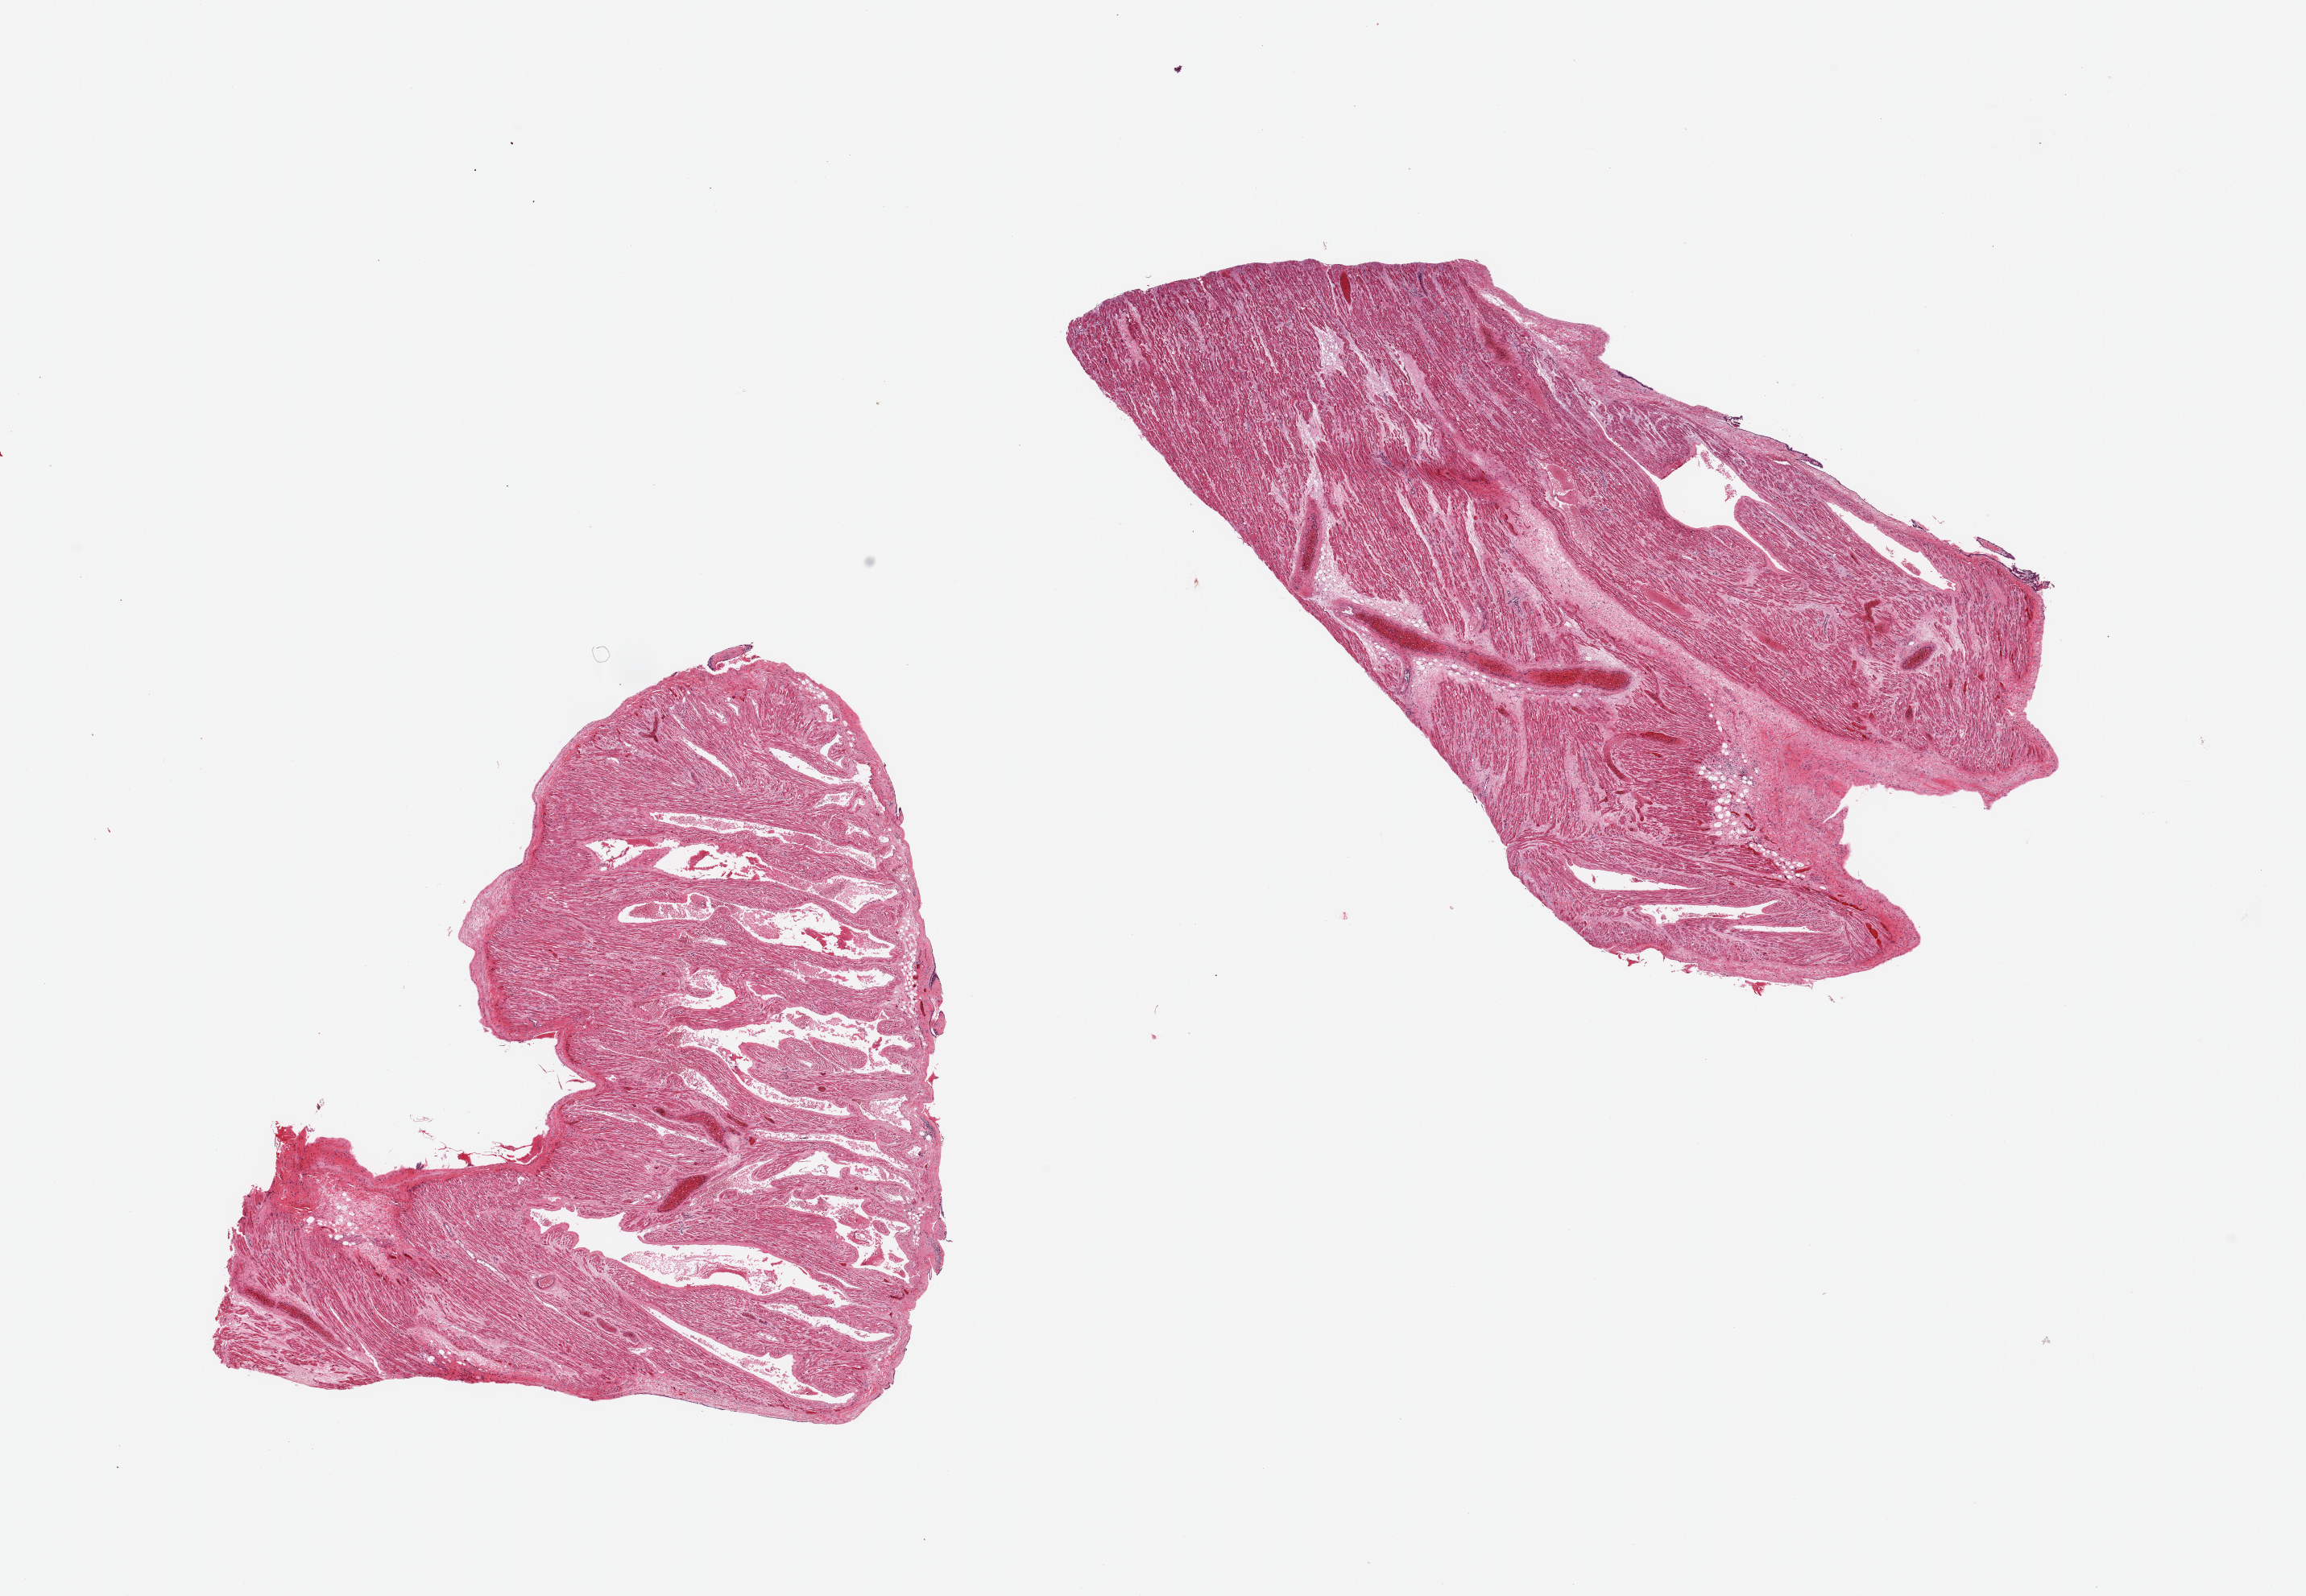
Whole-slide image, H&E stain, brightfield — shown as a low-resolution overview of the whole scanned area (about 22.6 x 15.7 mm, from a 20x scan); PAXgene-fixed, paraffin-embedded tissue; section of auricular appendage (target tissue); tissue donor sample. Male donor.
* review note (as recorded): 2 pieces, no abnormalities